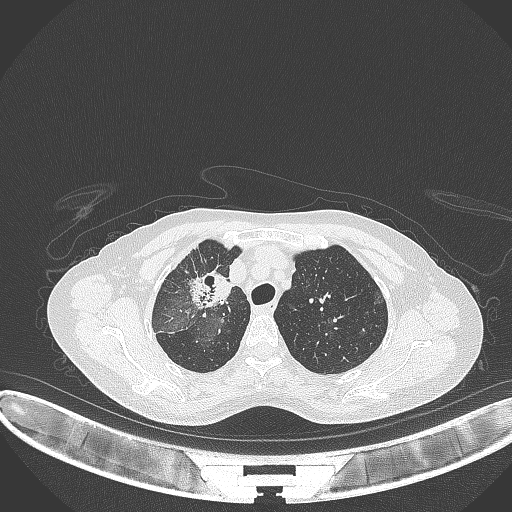
Chest CT, one axial slice. Slice 254 of 284 in the series (ordered by position). Reconstruction kernel B70f. Lung window (W 1500 / L -600 HU). 512 × 512 image matrix. Patient: female, 59 years. From the clinical record (not read from this slice): clinical TNM (as recorded): T3 N0 M0.
Annotated regions visible in this slice (rectangle marked by the reading radiologist):
- lung tumour (recorded histology: adenocarcinoma): bounding box (x1, y1, x2, y2) in pixels: (189, 270, 233, 311)